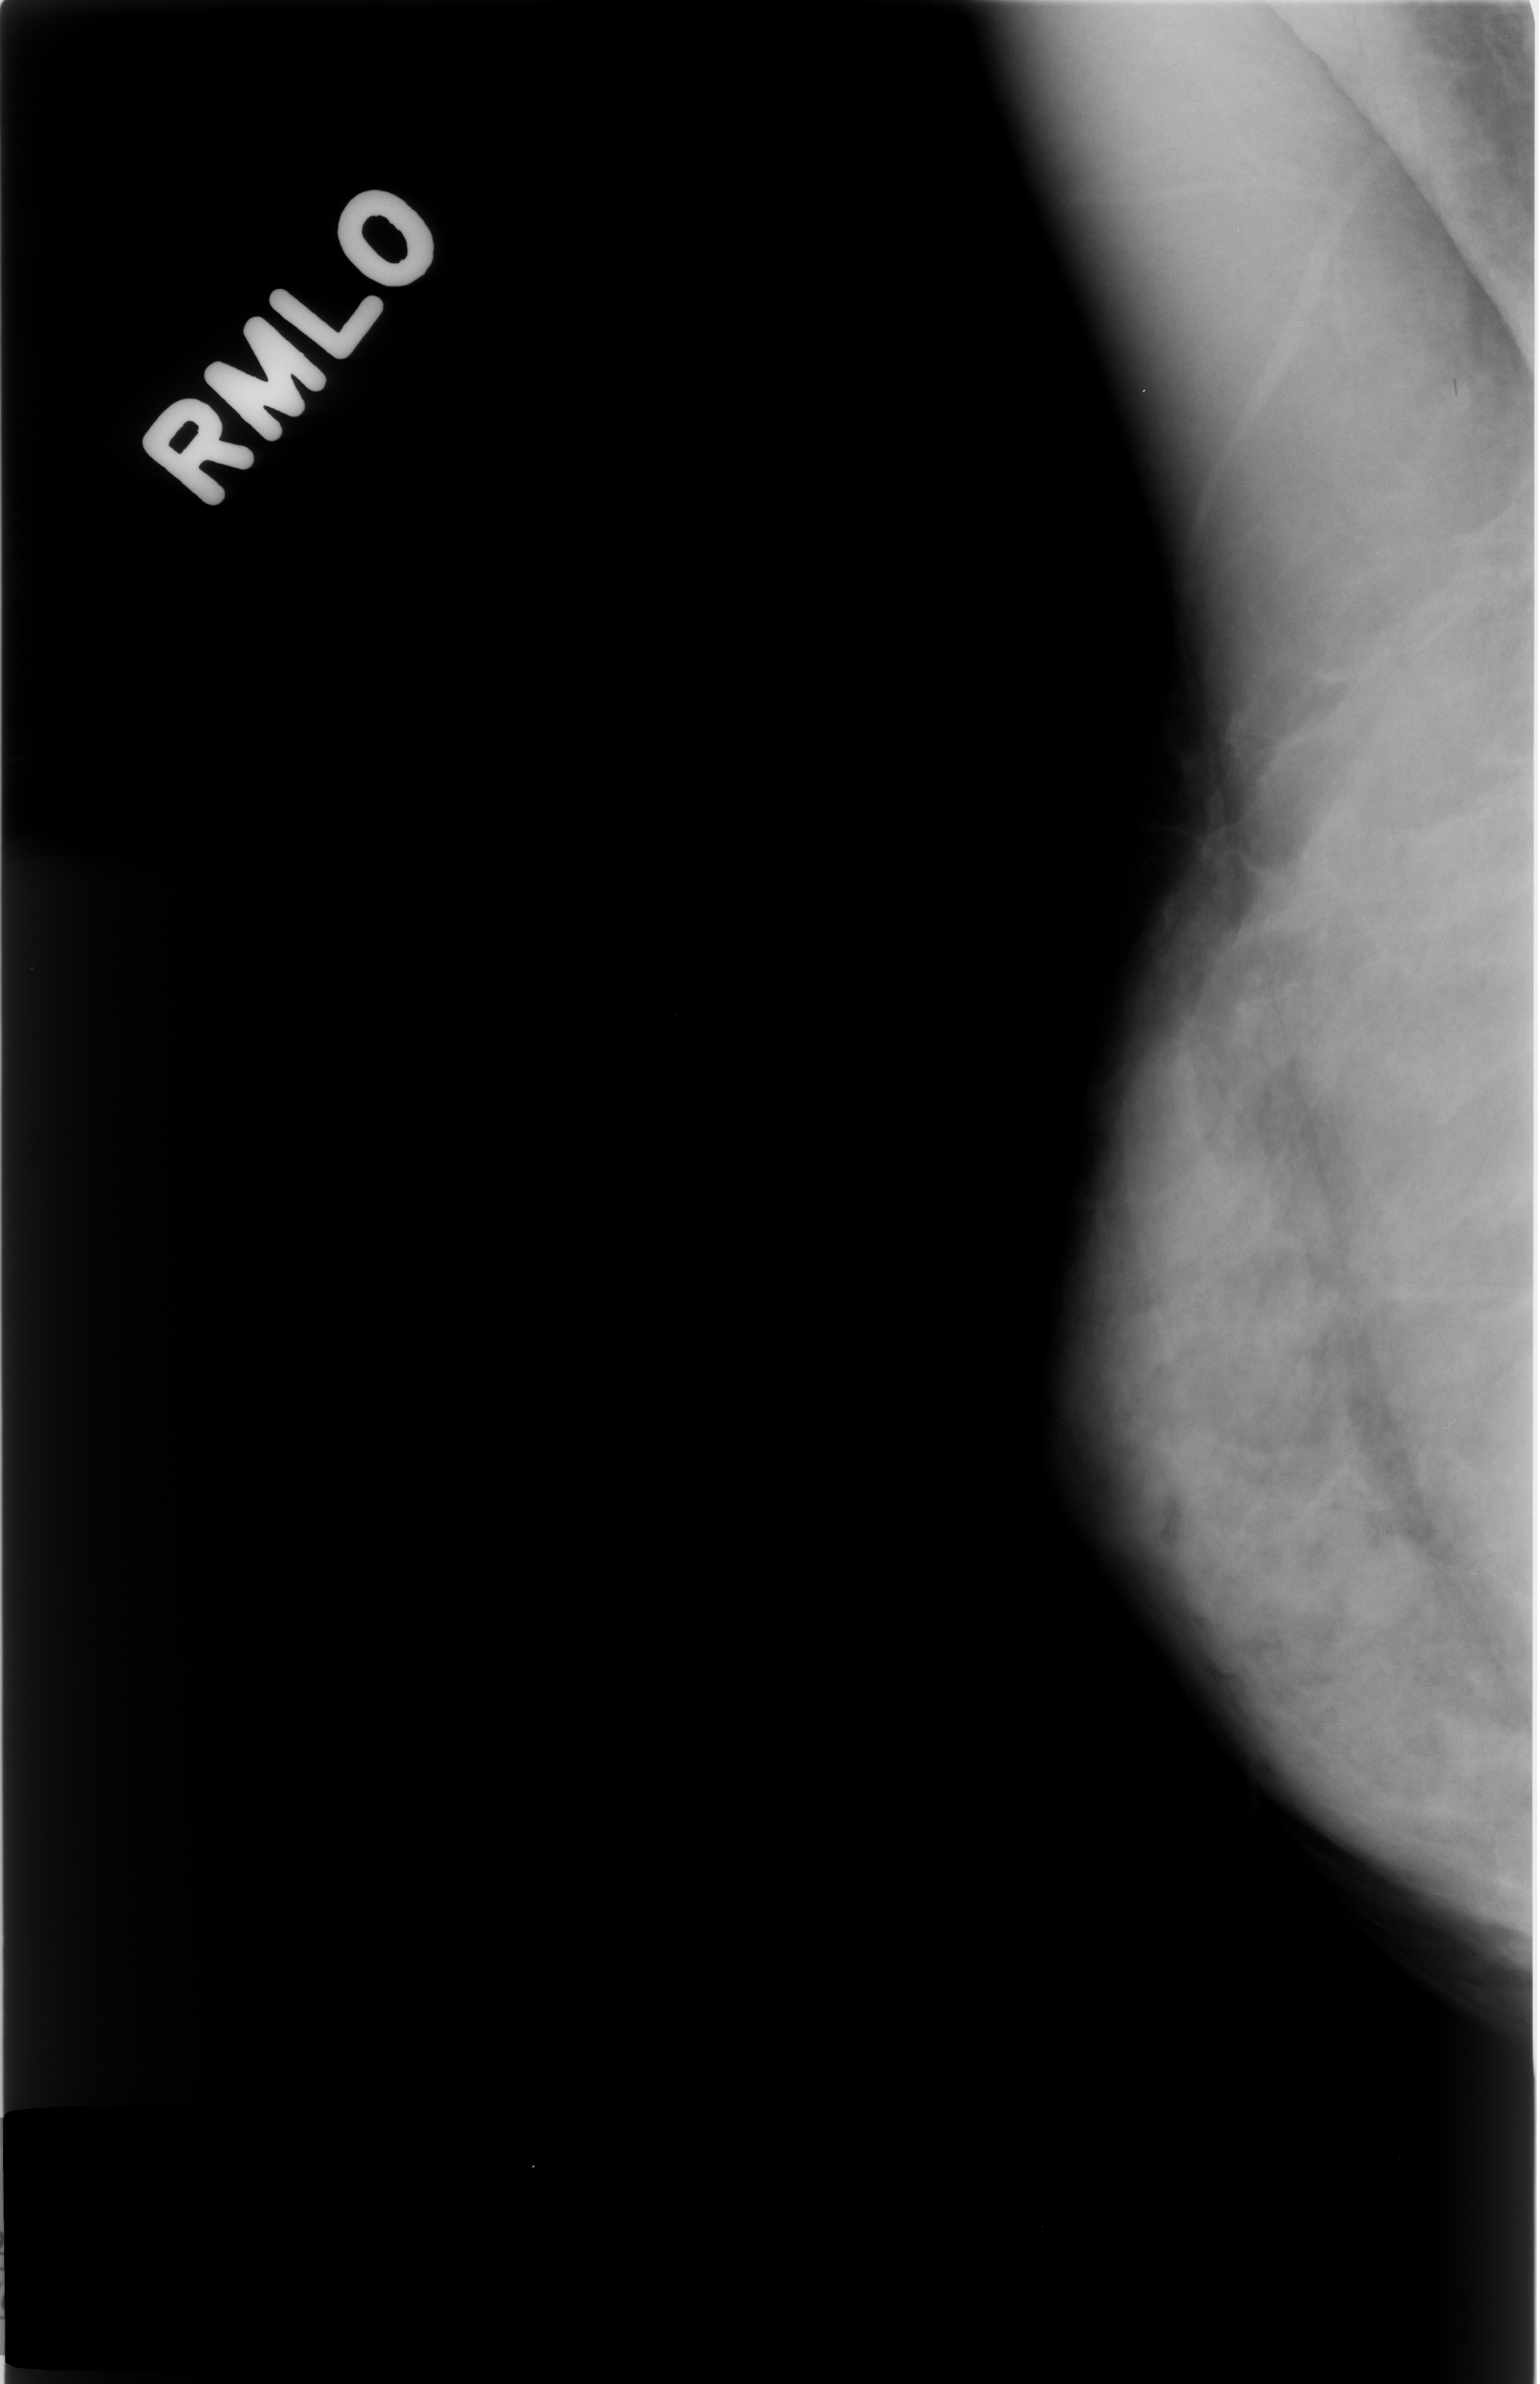
Digitized screen-film mammogram; right breast; mediolateral oblique (MLO) view; breast composition: extremely dense (BI-RADS density category 4 of 4); 1540 × 2384 image matrix.
Expert-marked regions of interest on this film, with their recorded descriptors:
- mass, shape oval, margins circumscribed; BI-RADS assessment category 3; benign; no additional work-up was recommended (outcome (as recorded, no biopsy): benign without callback): box from (x=1320, y=1513) to (x=1442, y=1643) px